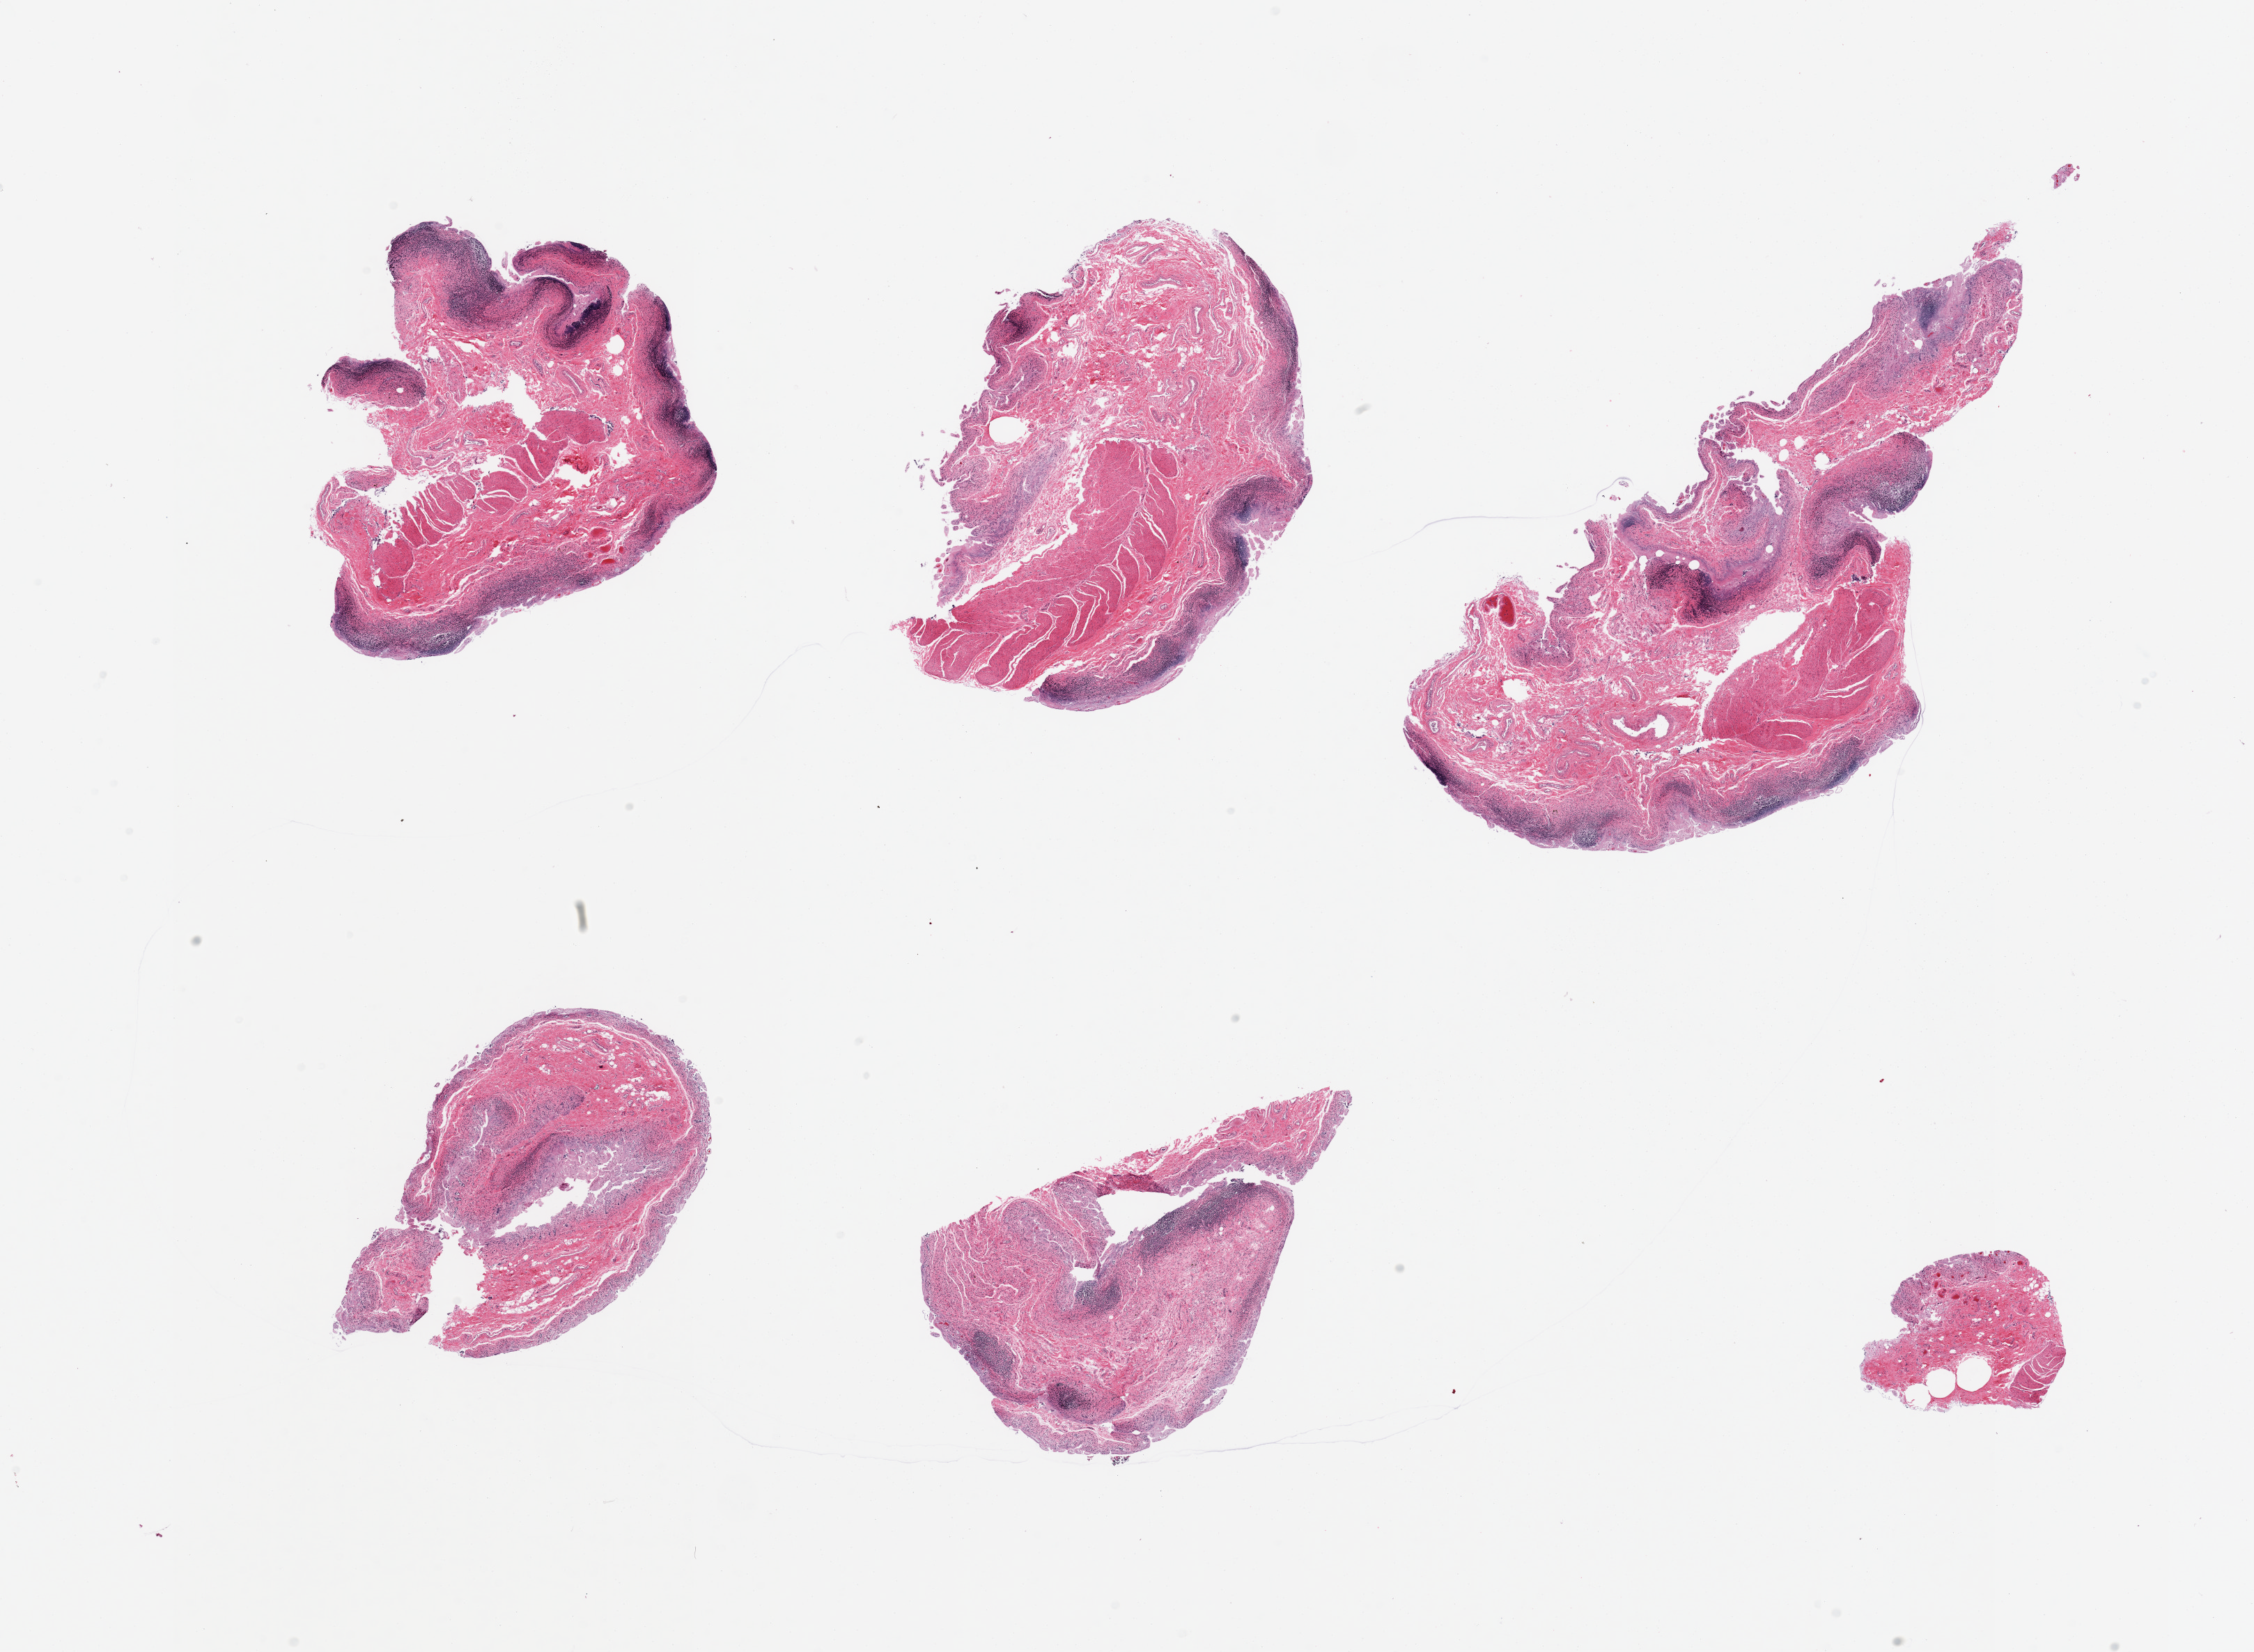
Haematoxylin and eosin whole-slide image — shown as a low-resolution overview of the whole scanned area (about 25.6 x 18.8 mm, from a 20x scan), PAXgene-fixed paraffin-embedded (PFPE) section, section of ileum (target tissue), tissue donor sample.
* pathologist's review note for this sample: 6 pieces; autolyzed mucosa, preserved muscularis and residual target lymphoid aggregates